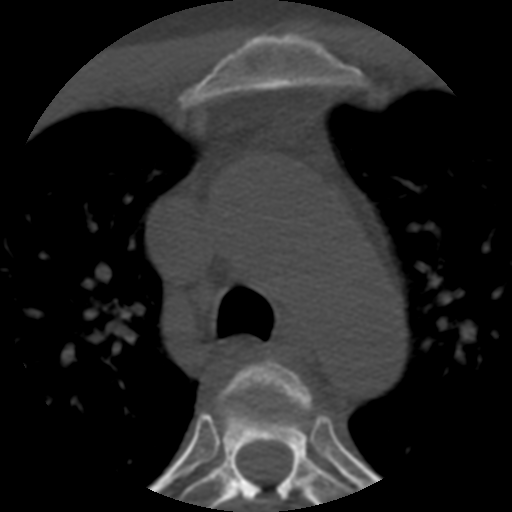
CT including the spine, one axial slice. Slice 401 of 508 in the series (ordered by position). Bone window (W 1800 / L 400 HU). 1.25 mm slice thickness. 512 × 512 image matrix, field of view 160 × 160 mm. Patient age 57 years. Case-level facts recorded for this patient, not image findings: primary cancer: prostate.
Outlined on this slice (semi-automatic segmentation, software-assisted and operator-edited):
- T3 vertebra: bounding box (x1, y1, x2, y2) in pixels: (216, 360, 312, 505)
- T4 vertebra: (179, 414, 354, 512)